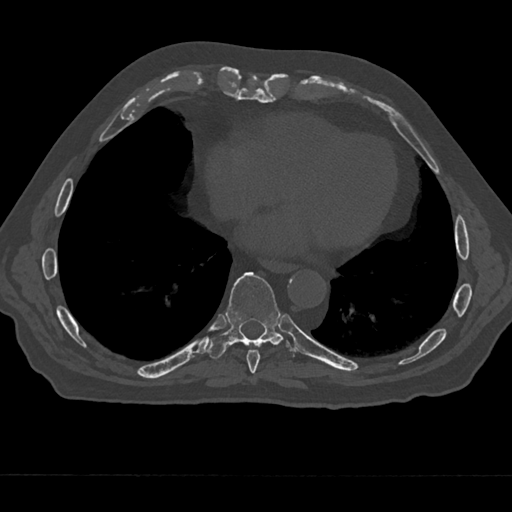
CT including the spine, one axial slice; position 280 of 797 along the scan axis; 120 kVp; bone window (W 1800 / L 400 HU); 512 × 512 image matrix, field of view 377 × 377 mm. Patient: male, 75 years. Case-level facts recorded for this patient, not image findings: primary cancer: renal; vertebrae with lytic lesions (as recorded): T4.
Annotated regions visible in this slice (semi-automatically segmented with operator editing):
- T8 vertebra: box from (x=246, y=349) to (x=260, y=373) px
- T9 vertebra: (x=207, y=272)–(x=296, y=359)